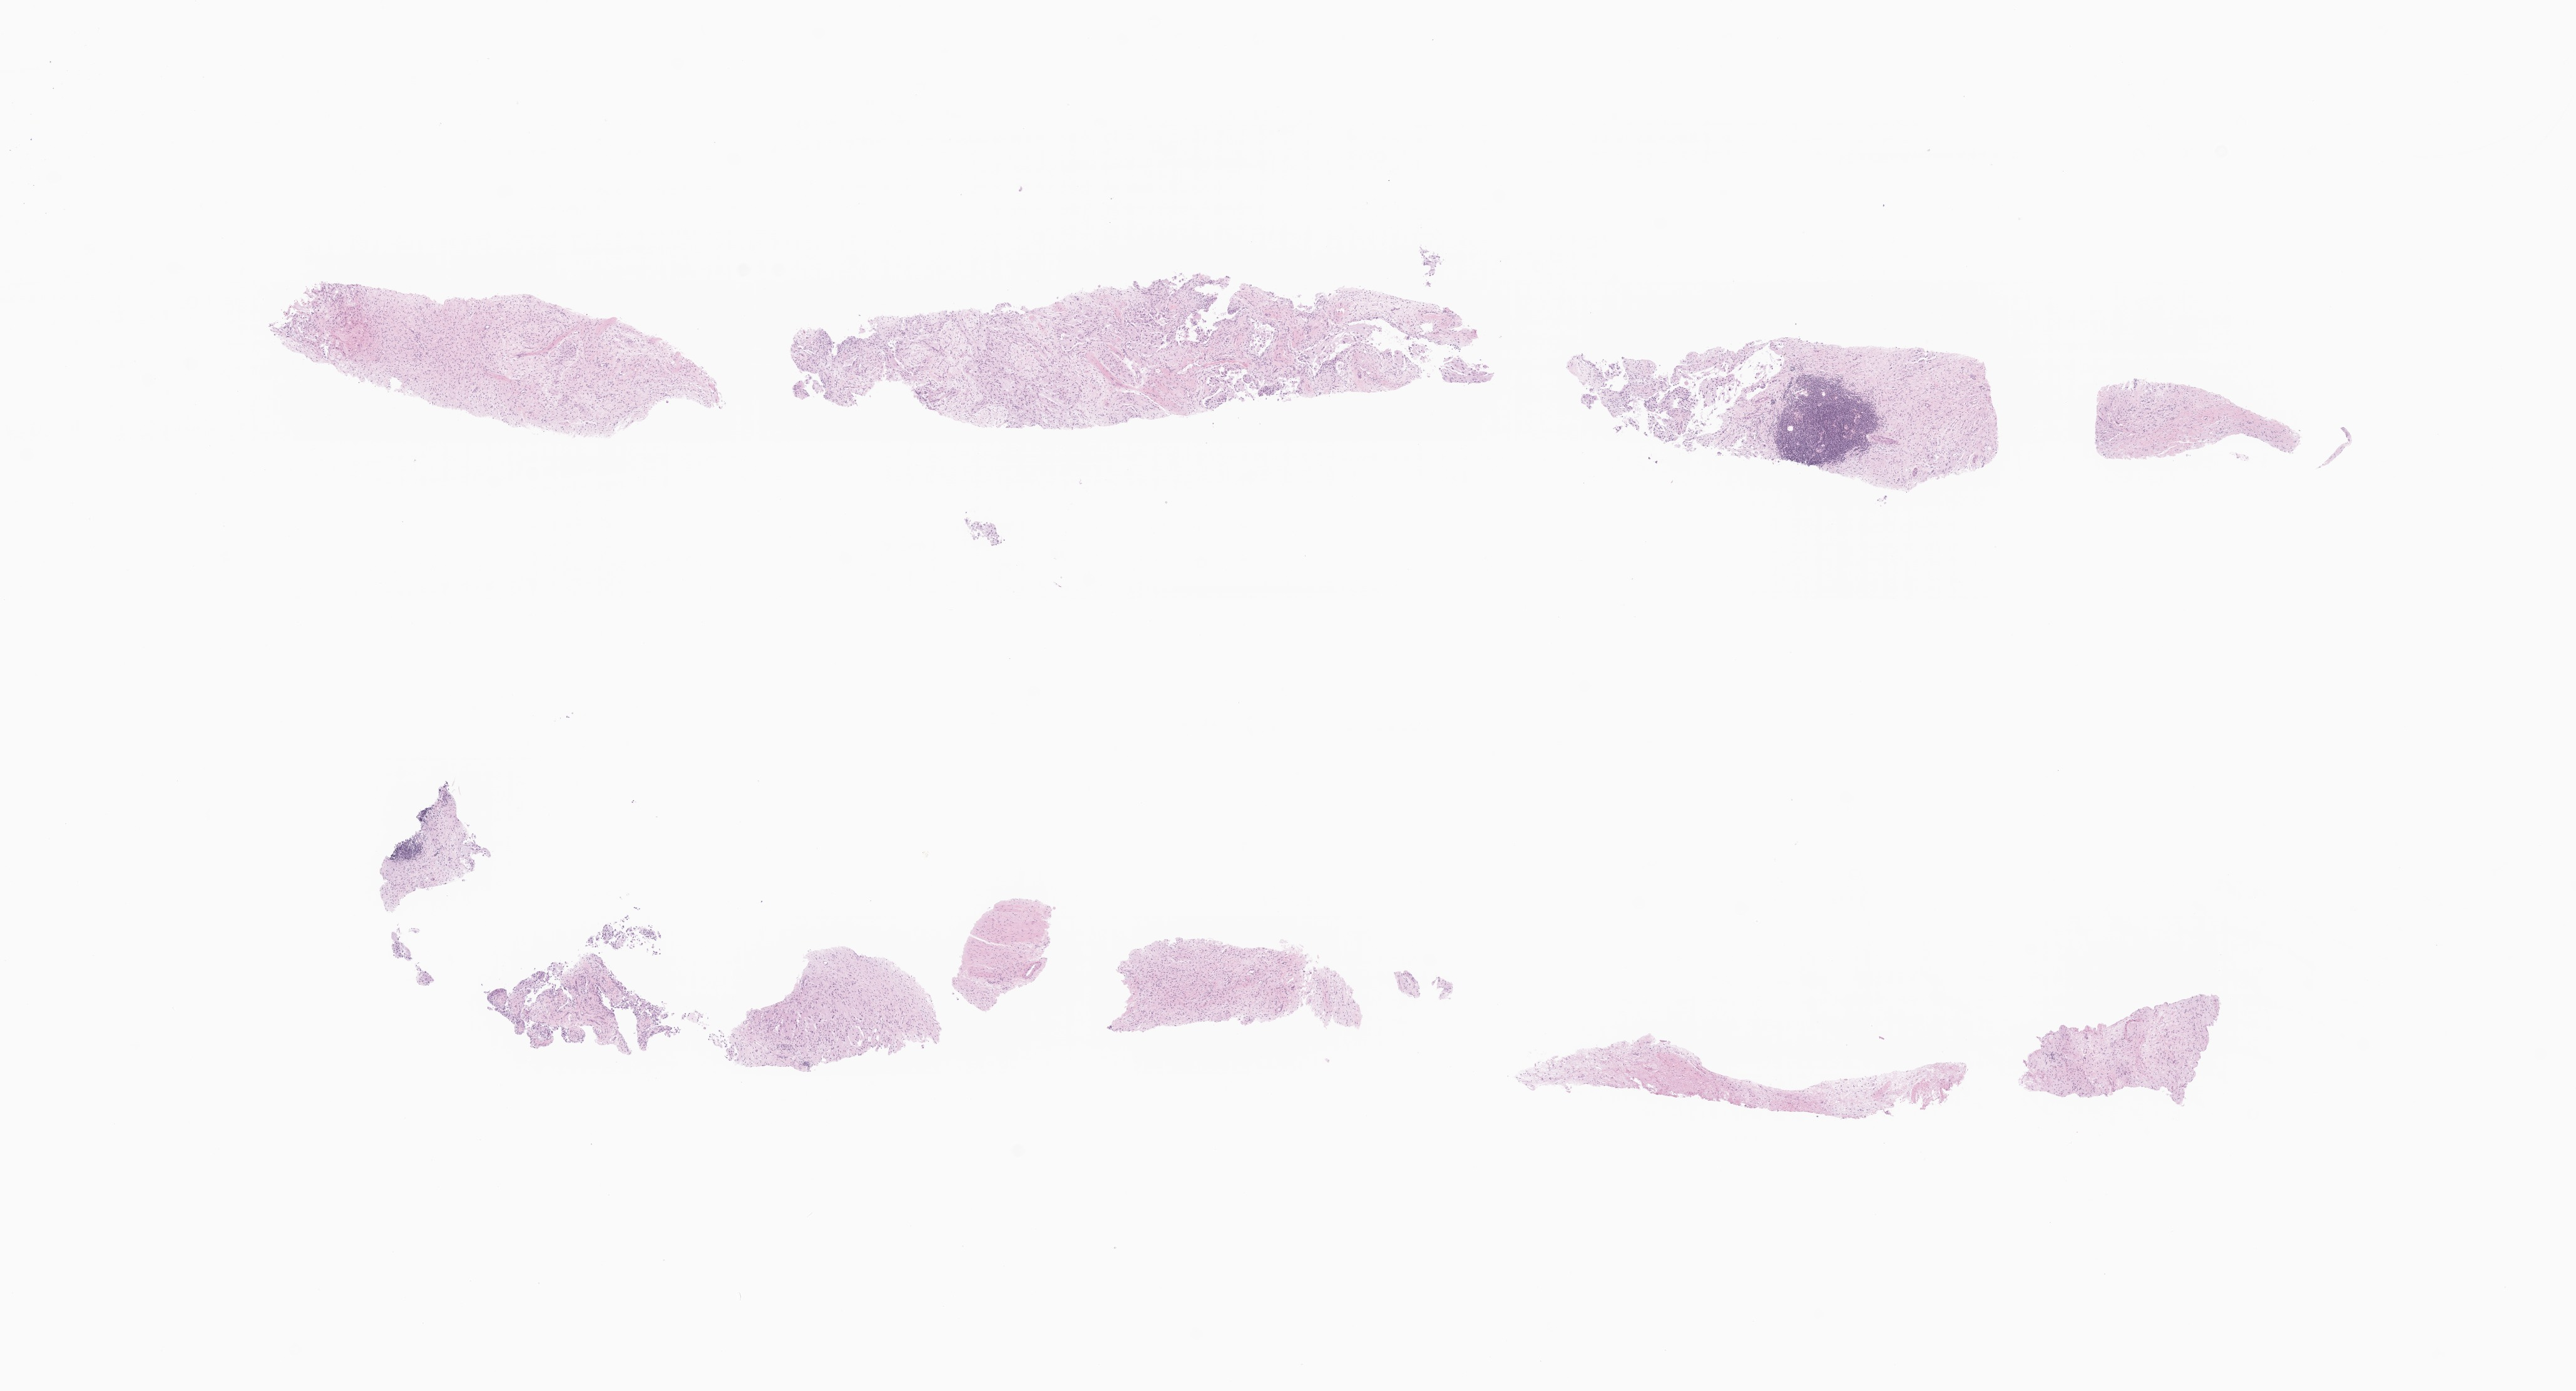
Digitized haematoxylin and eosin-stained section of tumor tissue from the abdominal lymph node, shown as a low-resolution overview of the whole scanned area (about 17.4 x 9.4 mm), formalin-fixed, paraffin-embedded (FFPE) tissue. Patient: female, age 35 months (2 years 11 months).
Recorded diagnosis: Neuroblastoma, NOS.